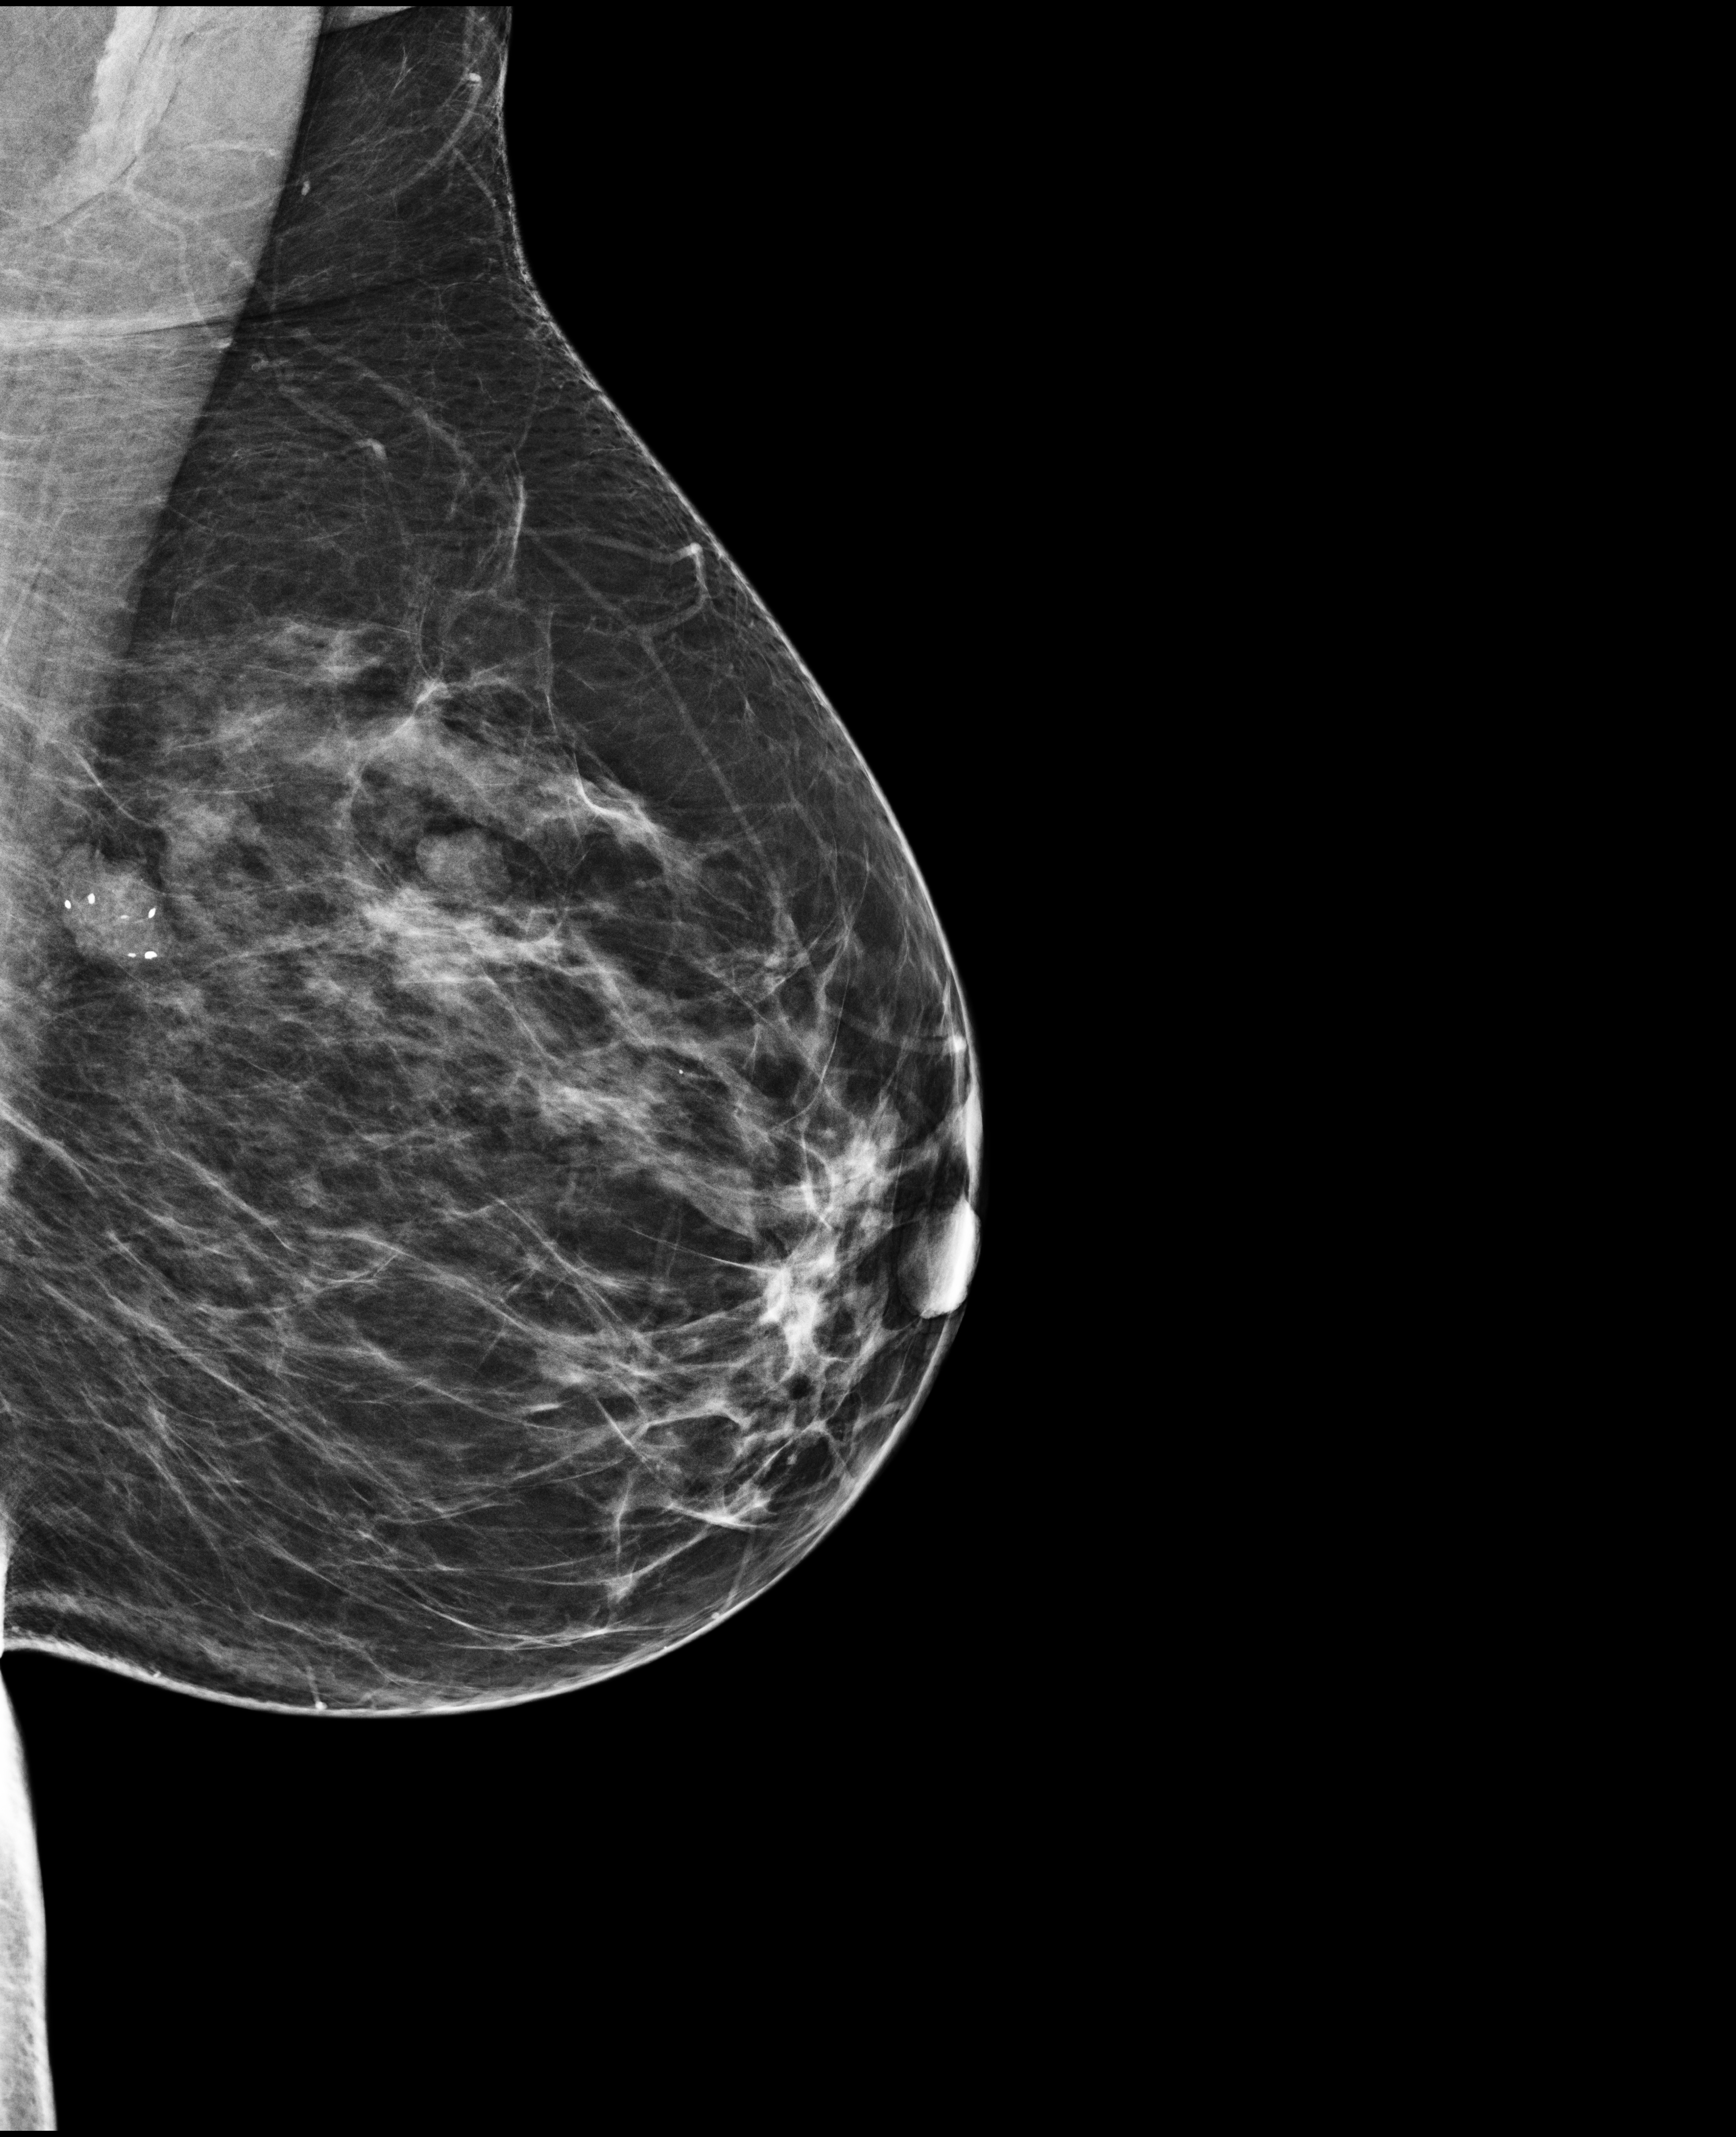
Screening examination; system: Selenia Dimensions. Female patient, age 64 years.
Image type: full-field digital mammogram. Breast: left. Projection: mediolateral oblique (MLO) view. Breast density at the screening exam (both breasts): heterogeneously dense (BI-RADS density category c). Final BI-RADS category for the screening round (tomosynthesis exam, both breasts): category 2. Recall: no recall after this screen.